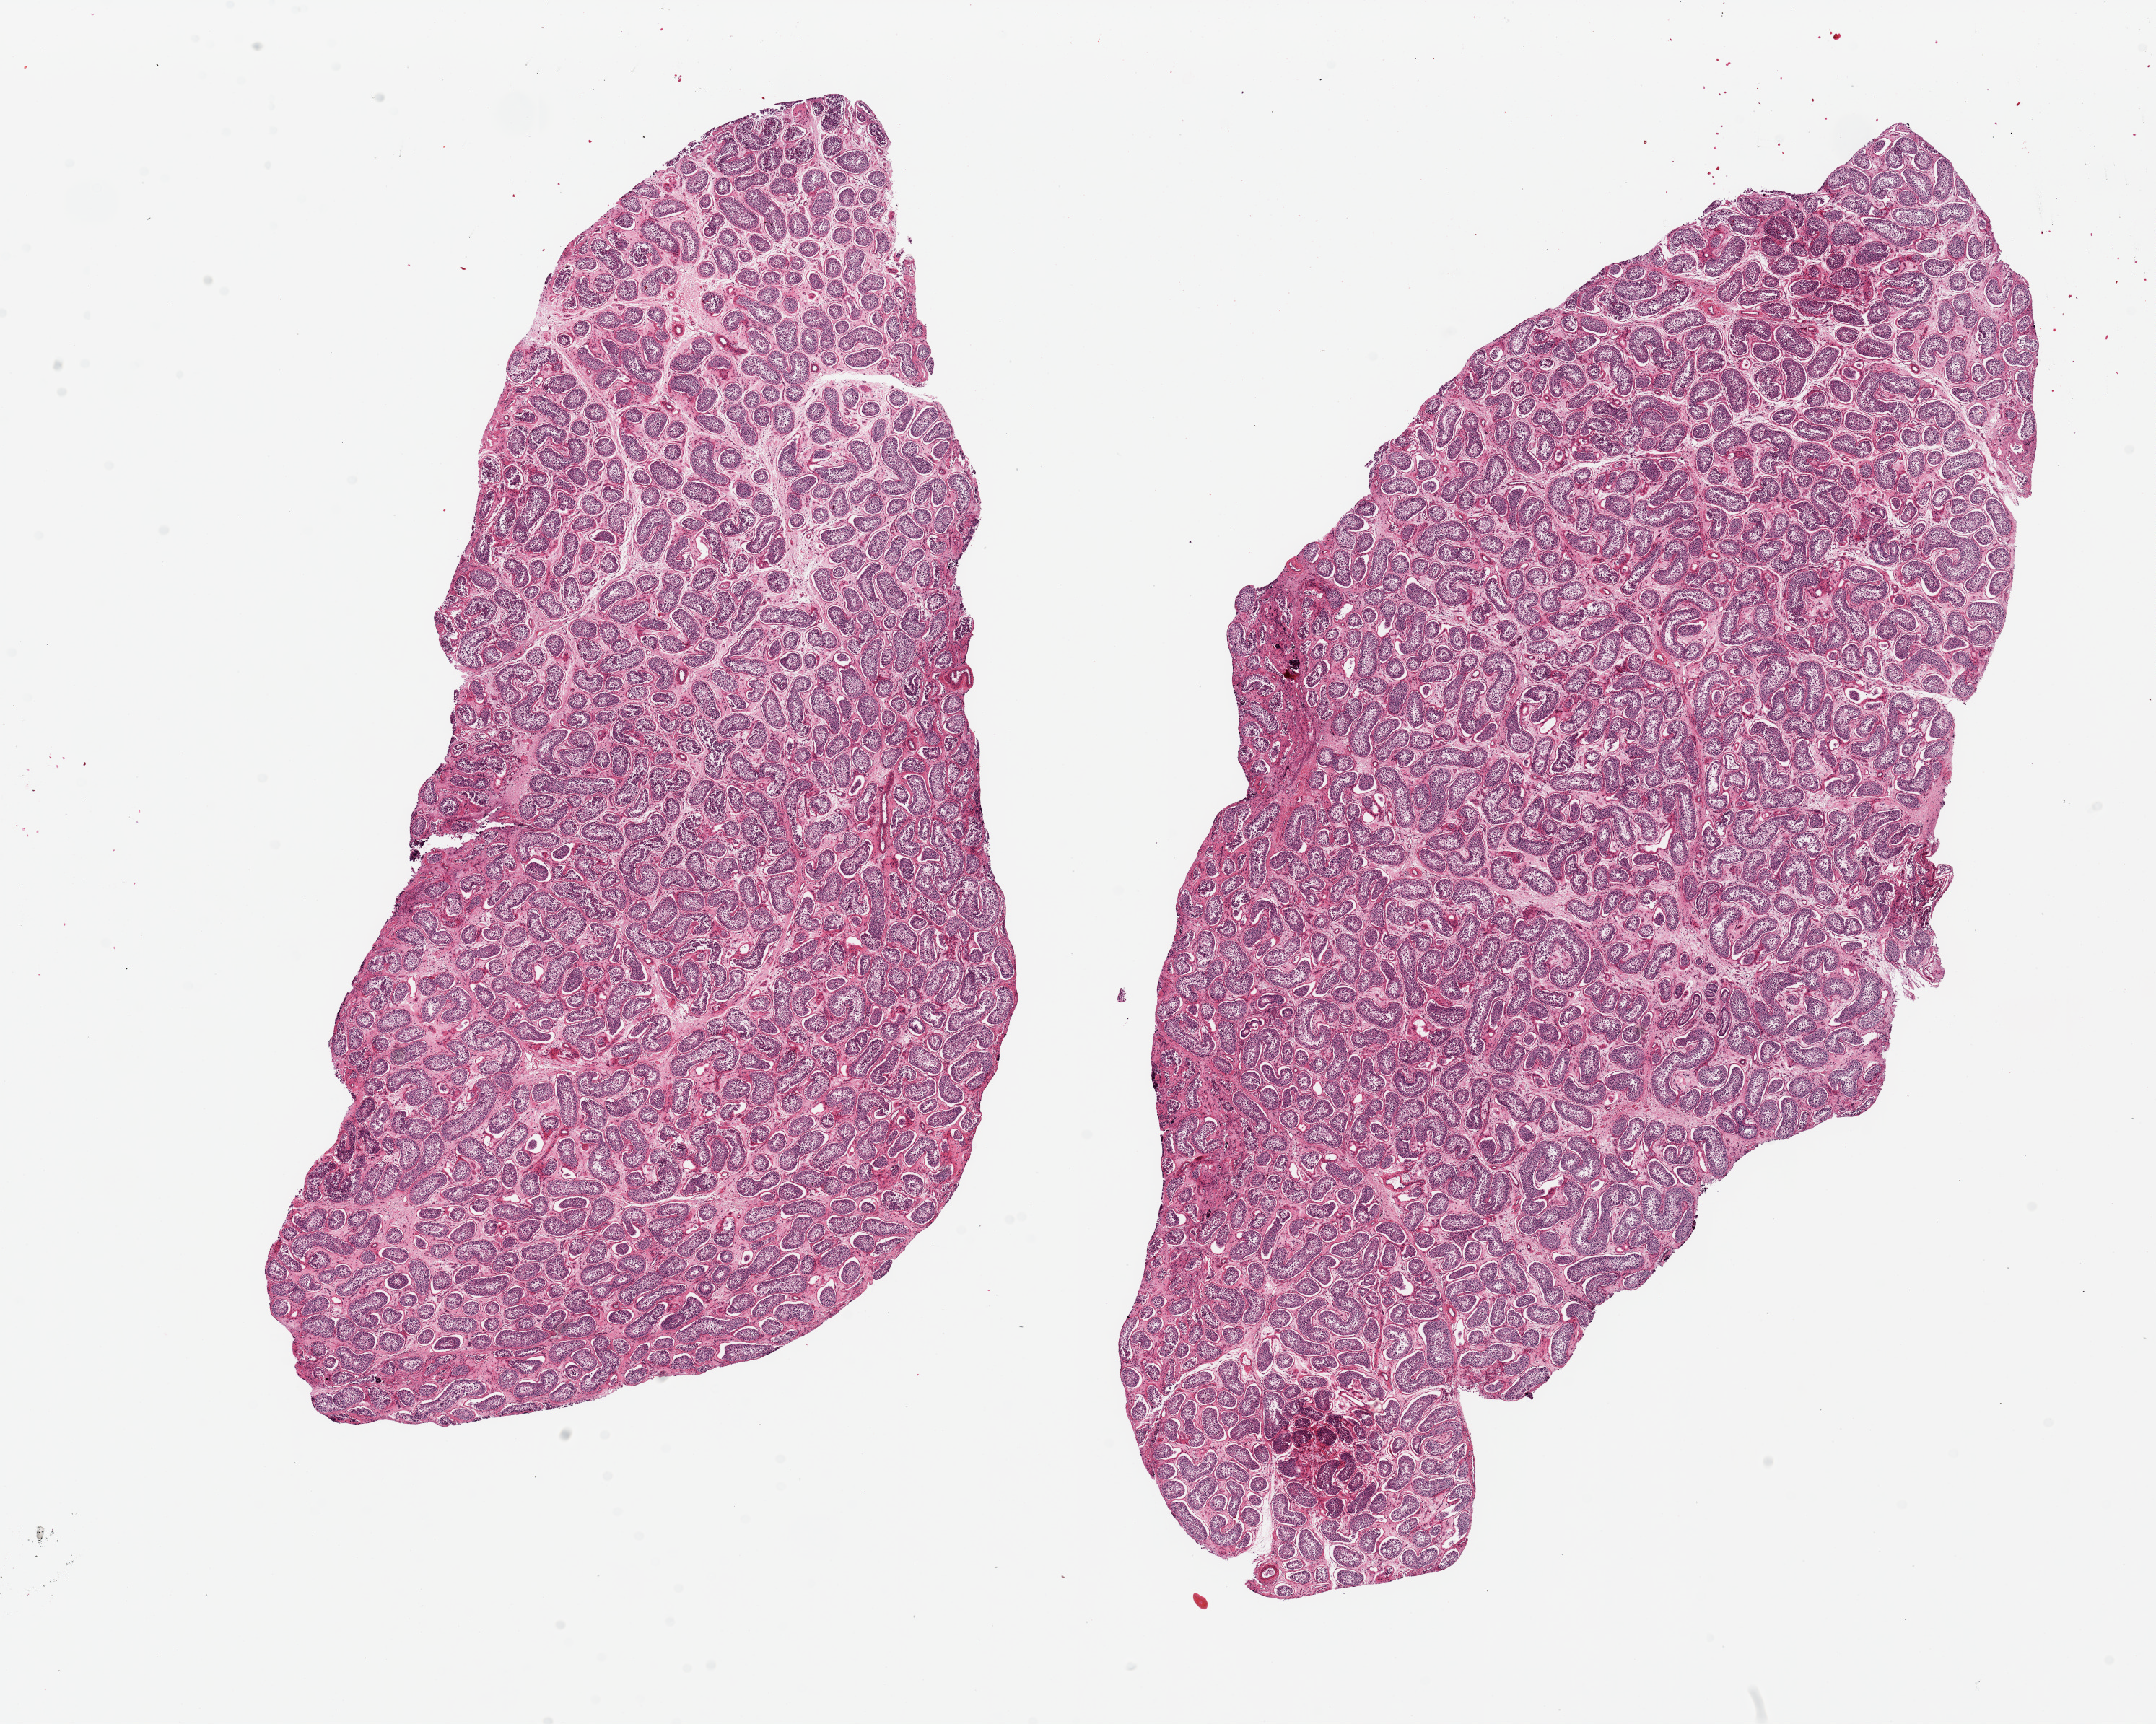
Haematoxylin and eosin whole-slide image, brightfield, a low-resolution overview of the entire scanned area, about 23.6 x 18.9 mm, PAXgene-fixed paraffin-embedded (PFPE) section, sampled site (target tissue): testis, tissue donor sample.
Reviewer comment on this tissue sample: 2 pieces ~14x8mm Spermatogeneisis is present.